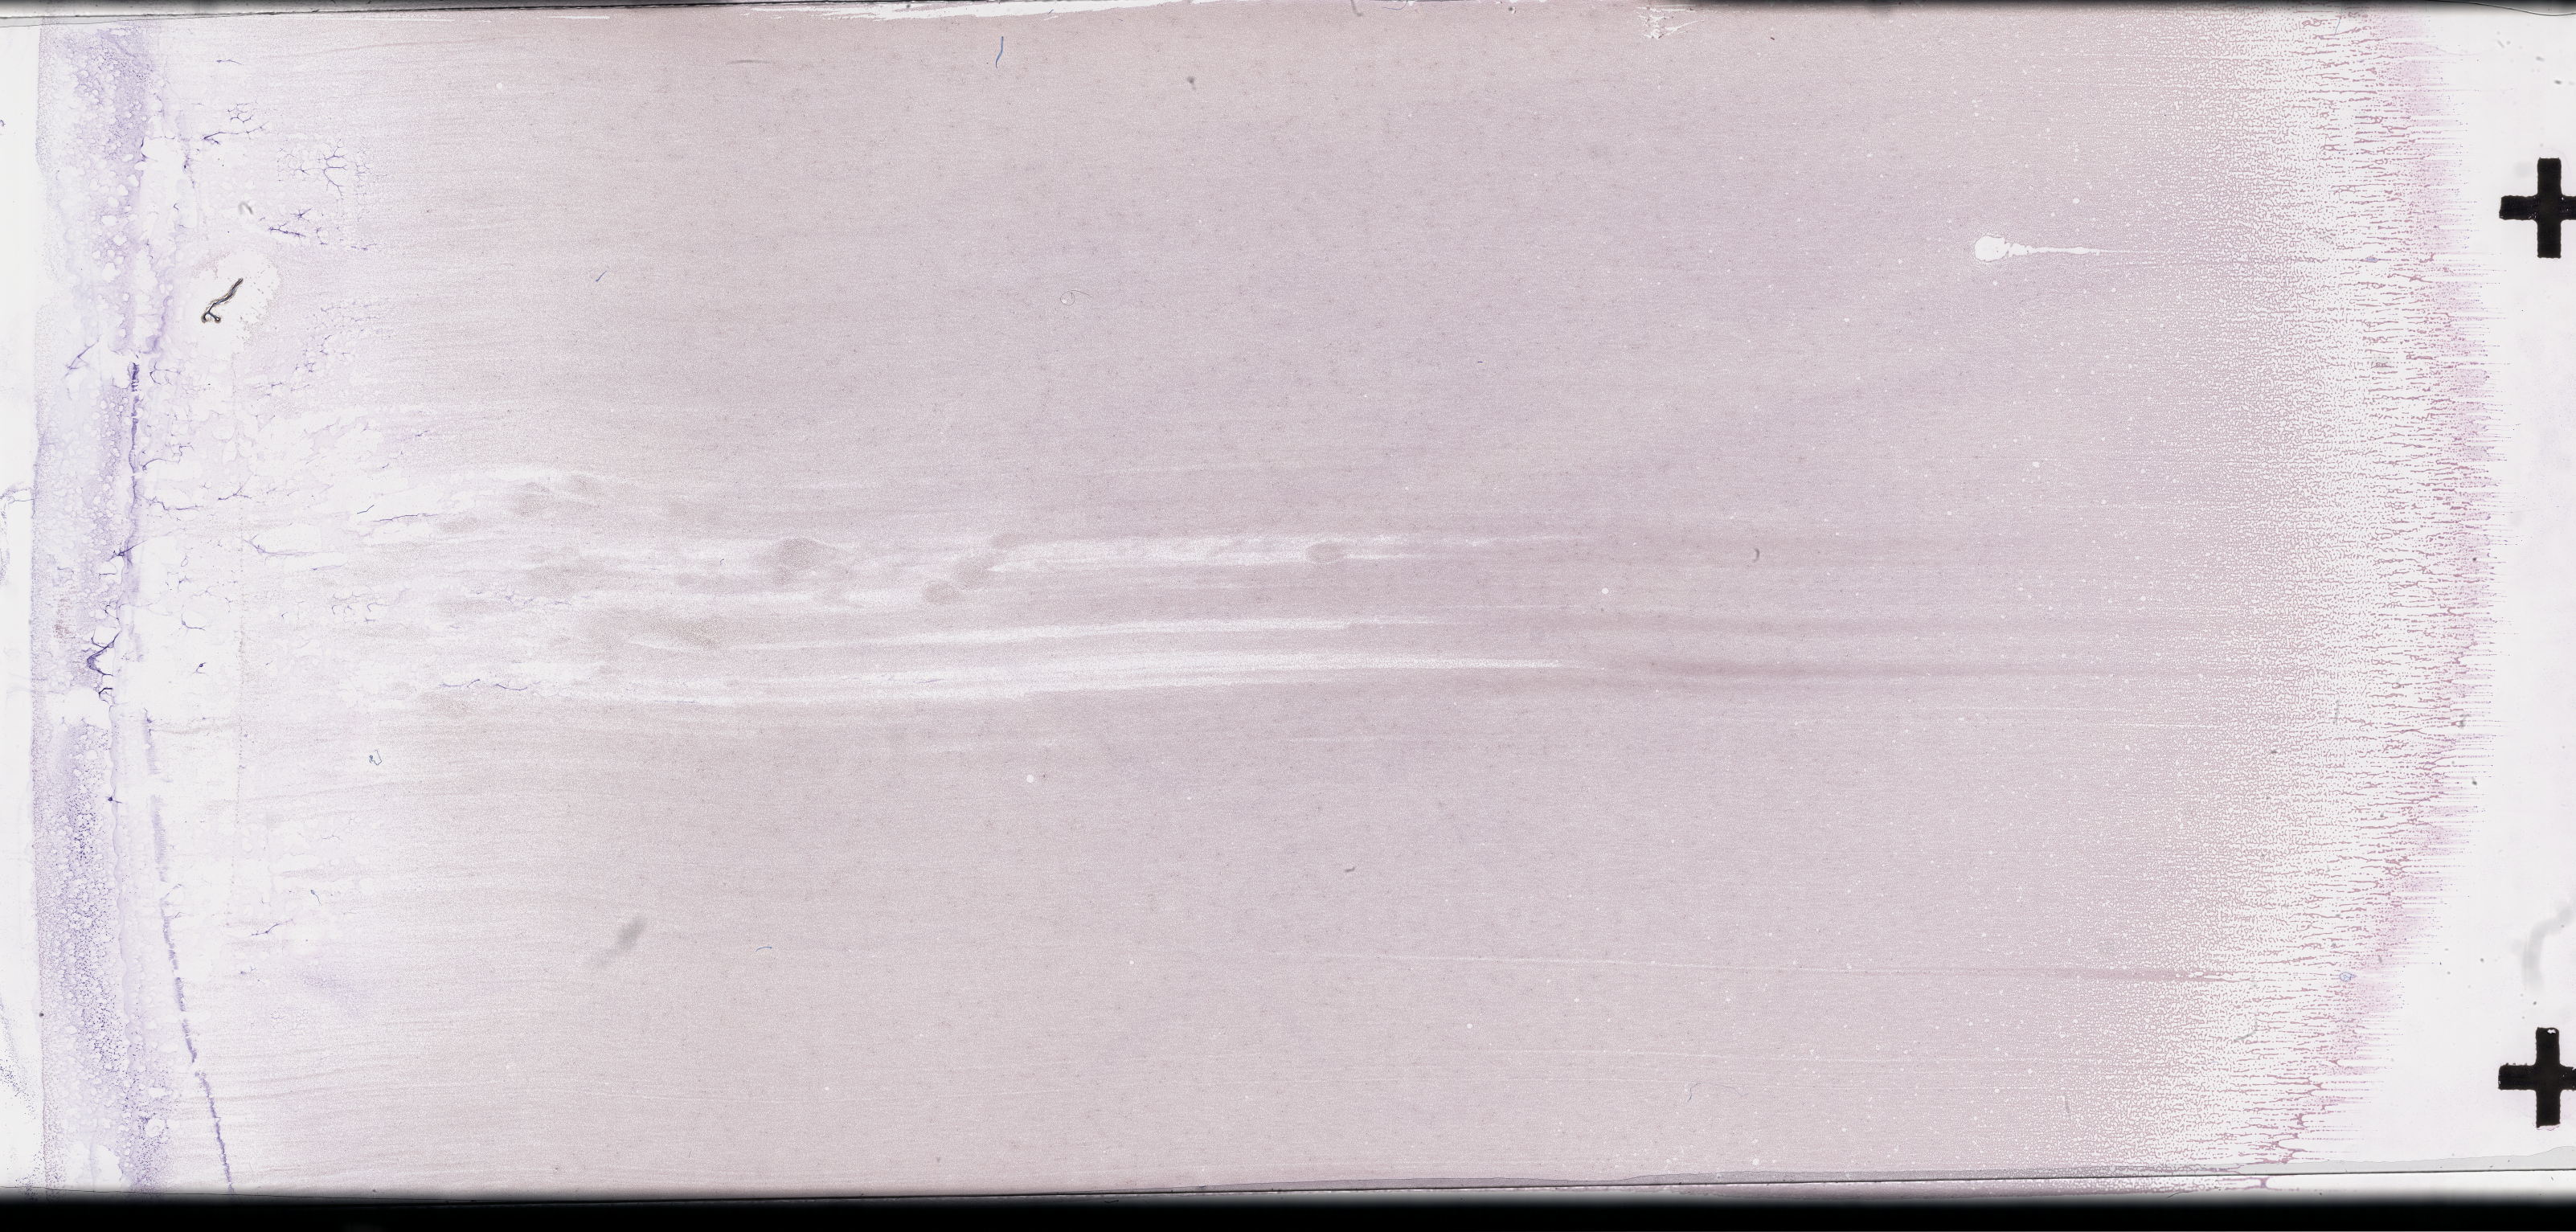
Whole-slide image of a whole blood smear, Wright–Giemsa stain — low-resolution overview of the scanned area, about 51.8 x 24.8 mm. Patient: female.
* from a patient with: Plasma Cell Myeloma